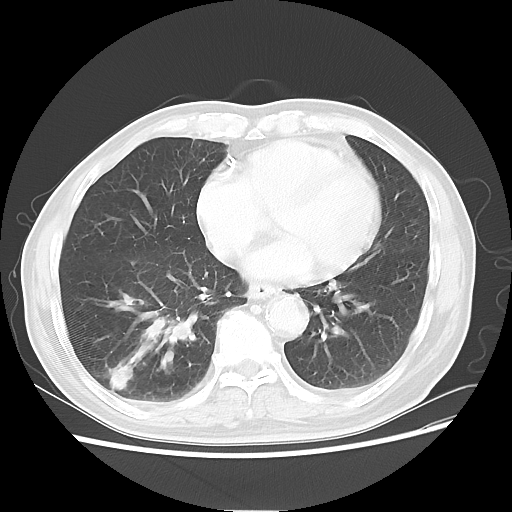
Chest CT, one axial slice. Position 21 of 58 along the scan axis. Reconstruction kernel LUNG. Lung window (W 1500 / L -600 HU). 5 mm slice thickness. 512 × 512 image matrix, field of view 360 × 360 mm. Male patient, age 74 years. From the clinical record (not read from this slice): clinical TNM (as recorded): T1c N1 M1.
Outlined on this slice (rectangle marked by the reading radiologist):
- lung tumour (recorded histology: adenocarcinoma): box from (x=128, y=286) to (x=201, y=369) px